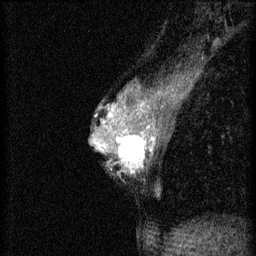
Breast MRI (dynamic contrast-enhanced), one sagittal slice. Slice 31 of 46 in the series (ordered by position). 3 images stored at this slice position (order not interpretable as contrast timing). 1.5 T. TE 4.2 ms, TR 8.2 ms. 256 × 256 image matrix, field of view 180 × 180 mm. Female patient, age 44 years.
Annotated regions visible in this slice (semi-automatic segmentation, software-assisted and operator-edited):
- analysis volume of interest (the breast-tissue region the enhancement analysis was run in; not a lesion): bounding box <110,128,156,175> (left, top, right, bottom; pixels)
- tumour enhancement mask (voxels above the 70 % enhancement threshold inside the analysis volume of interest): <111,128,156,173>